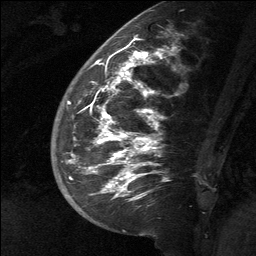
Breast MRI (dynamic contrast-enhanced), one sagittal slice. Slice 24 of 64 in the series (ordered by position). Dynamic contrast-enhanced study with each time point stored as its own series, time point 2 of 3 at this slice position (early post-contrast, ordered by acquisition time). 1.5 T. TE 4.8 ms, TR 27 ms. 2 mm slice thickness. 256 × 256 image matrix. Female patient, age 39 years. From the clinical record (not read from this slice): setting: breast cancer imaged before/during neoadjuvant chemotherapy; receptor status: HER2-positive.
Annotated regions visible in this slice (semi-automatic segmentation, software-assisted and operator-edited):
- analysis volume of interest (the breast-tissue region the enhancement analysis was run in; not a lesion): bounding box <58,40,170,217> (left, top, right, bottom; pixels)
- tumour enhancement mask (voxels above the 90 % enhancement threshold inside the analysis volume of interest): <68,50,163,199>